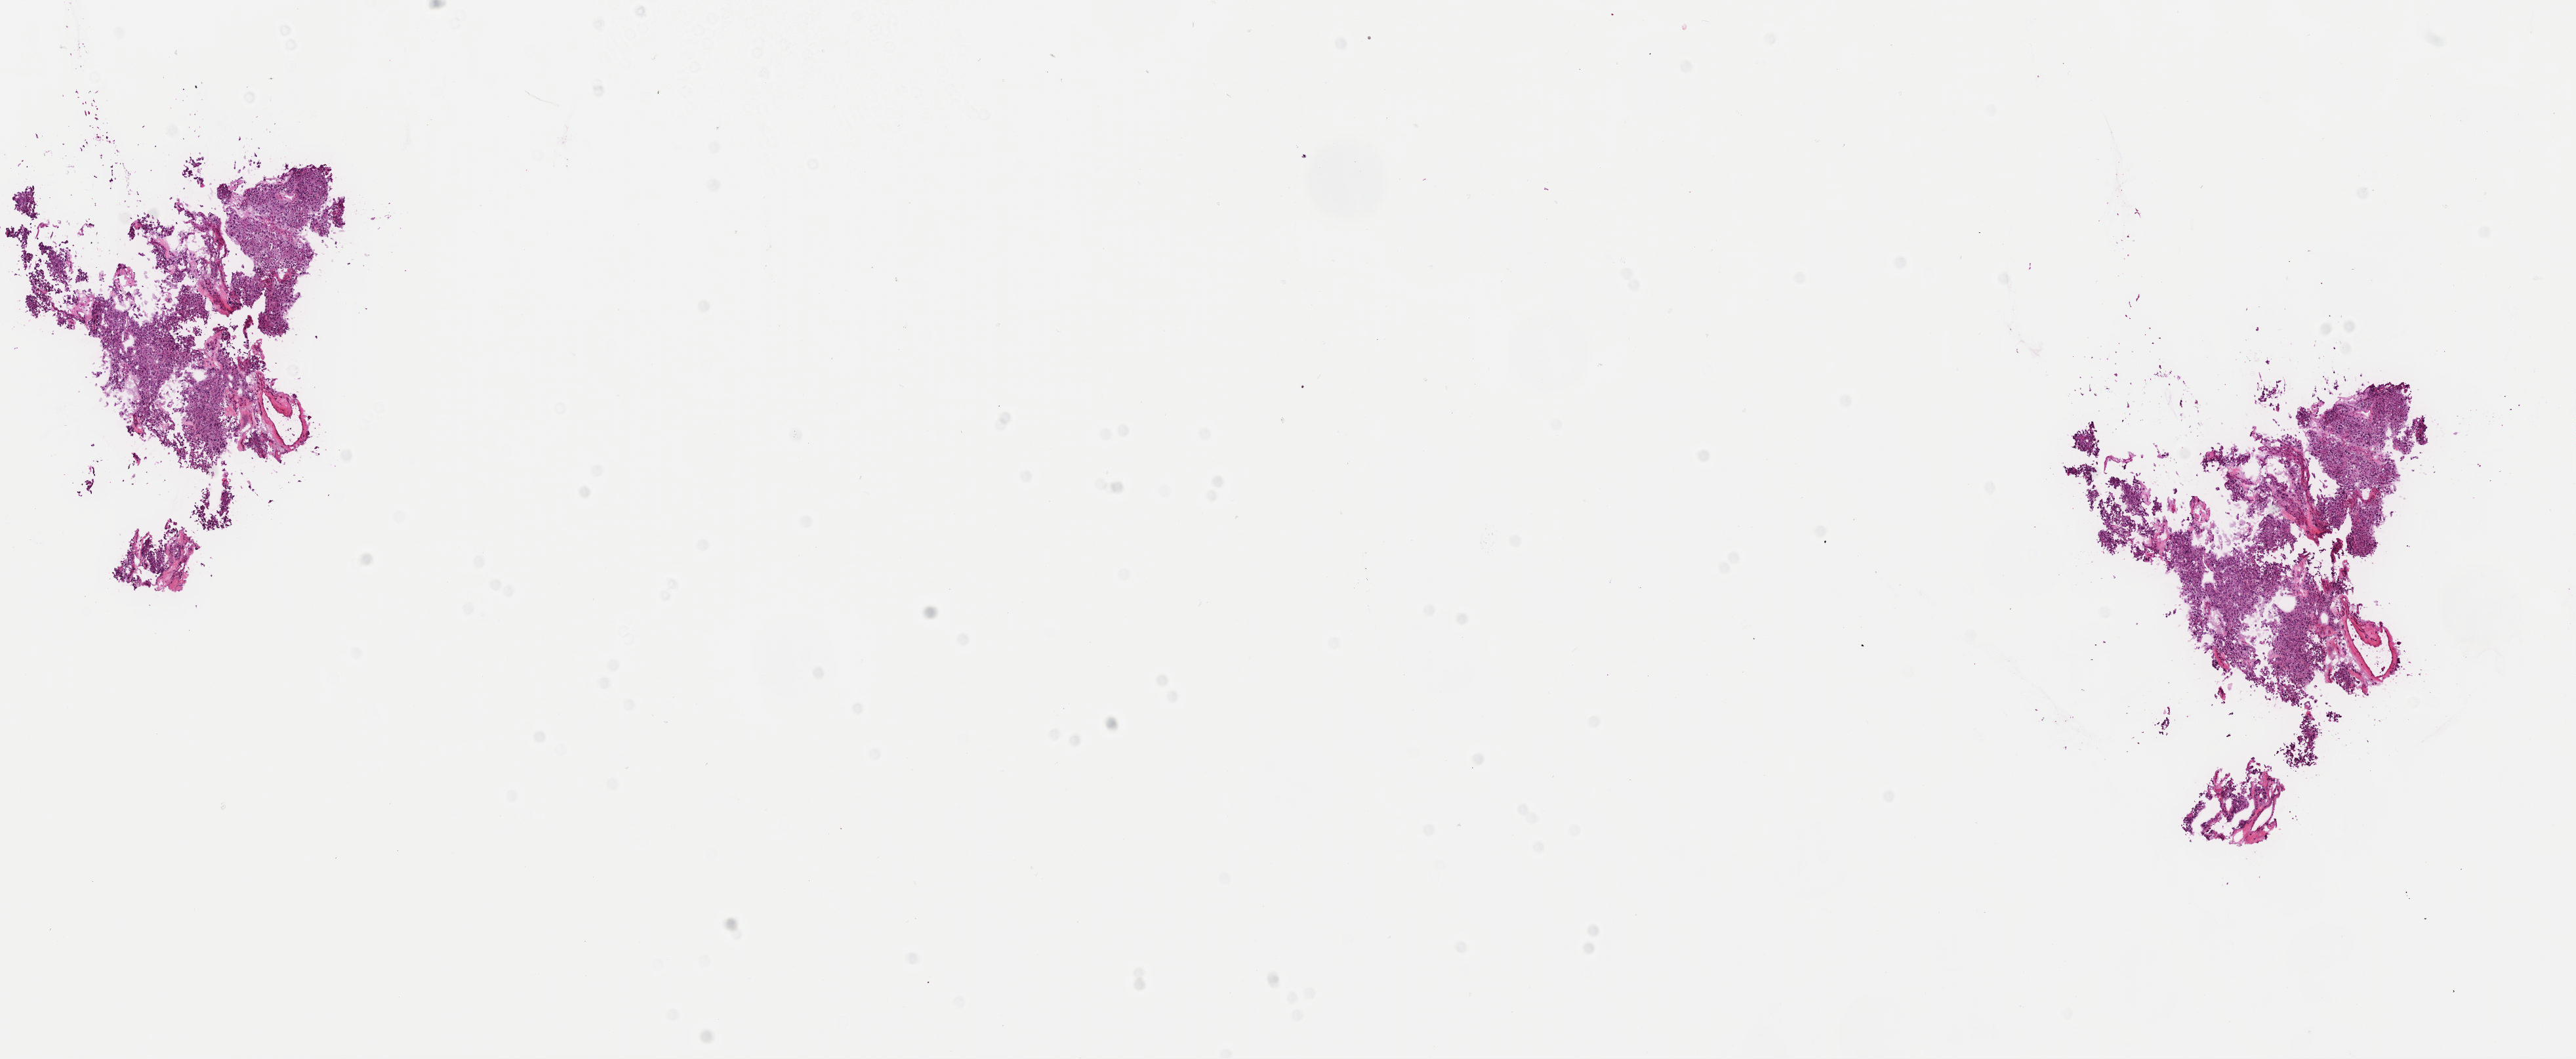
H&E-stained whole-slide image — a low-resolution overview of the entire scanned area, about 15.5 x 6.4 mm; frozen section; connective, subcutaneous and other soft tissues, primary tumour sample. Patient: female, age at initial diagnosis 50 years. Pathologist review of this section (percent, as recorded): tumour cells 100%, tumour nuclei 80%, normal cells 0%, stromal cells 0%, necrosis 0%. Infiltration values recorded for this section: lymphocyte infiltration 1%, monocyte infiltration 0%, neutrophil infiltration 0%.
• diagnosis: Extra-adrenal paraganglioma, NOS